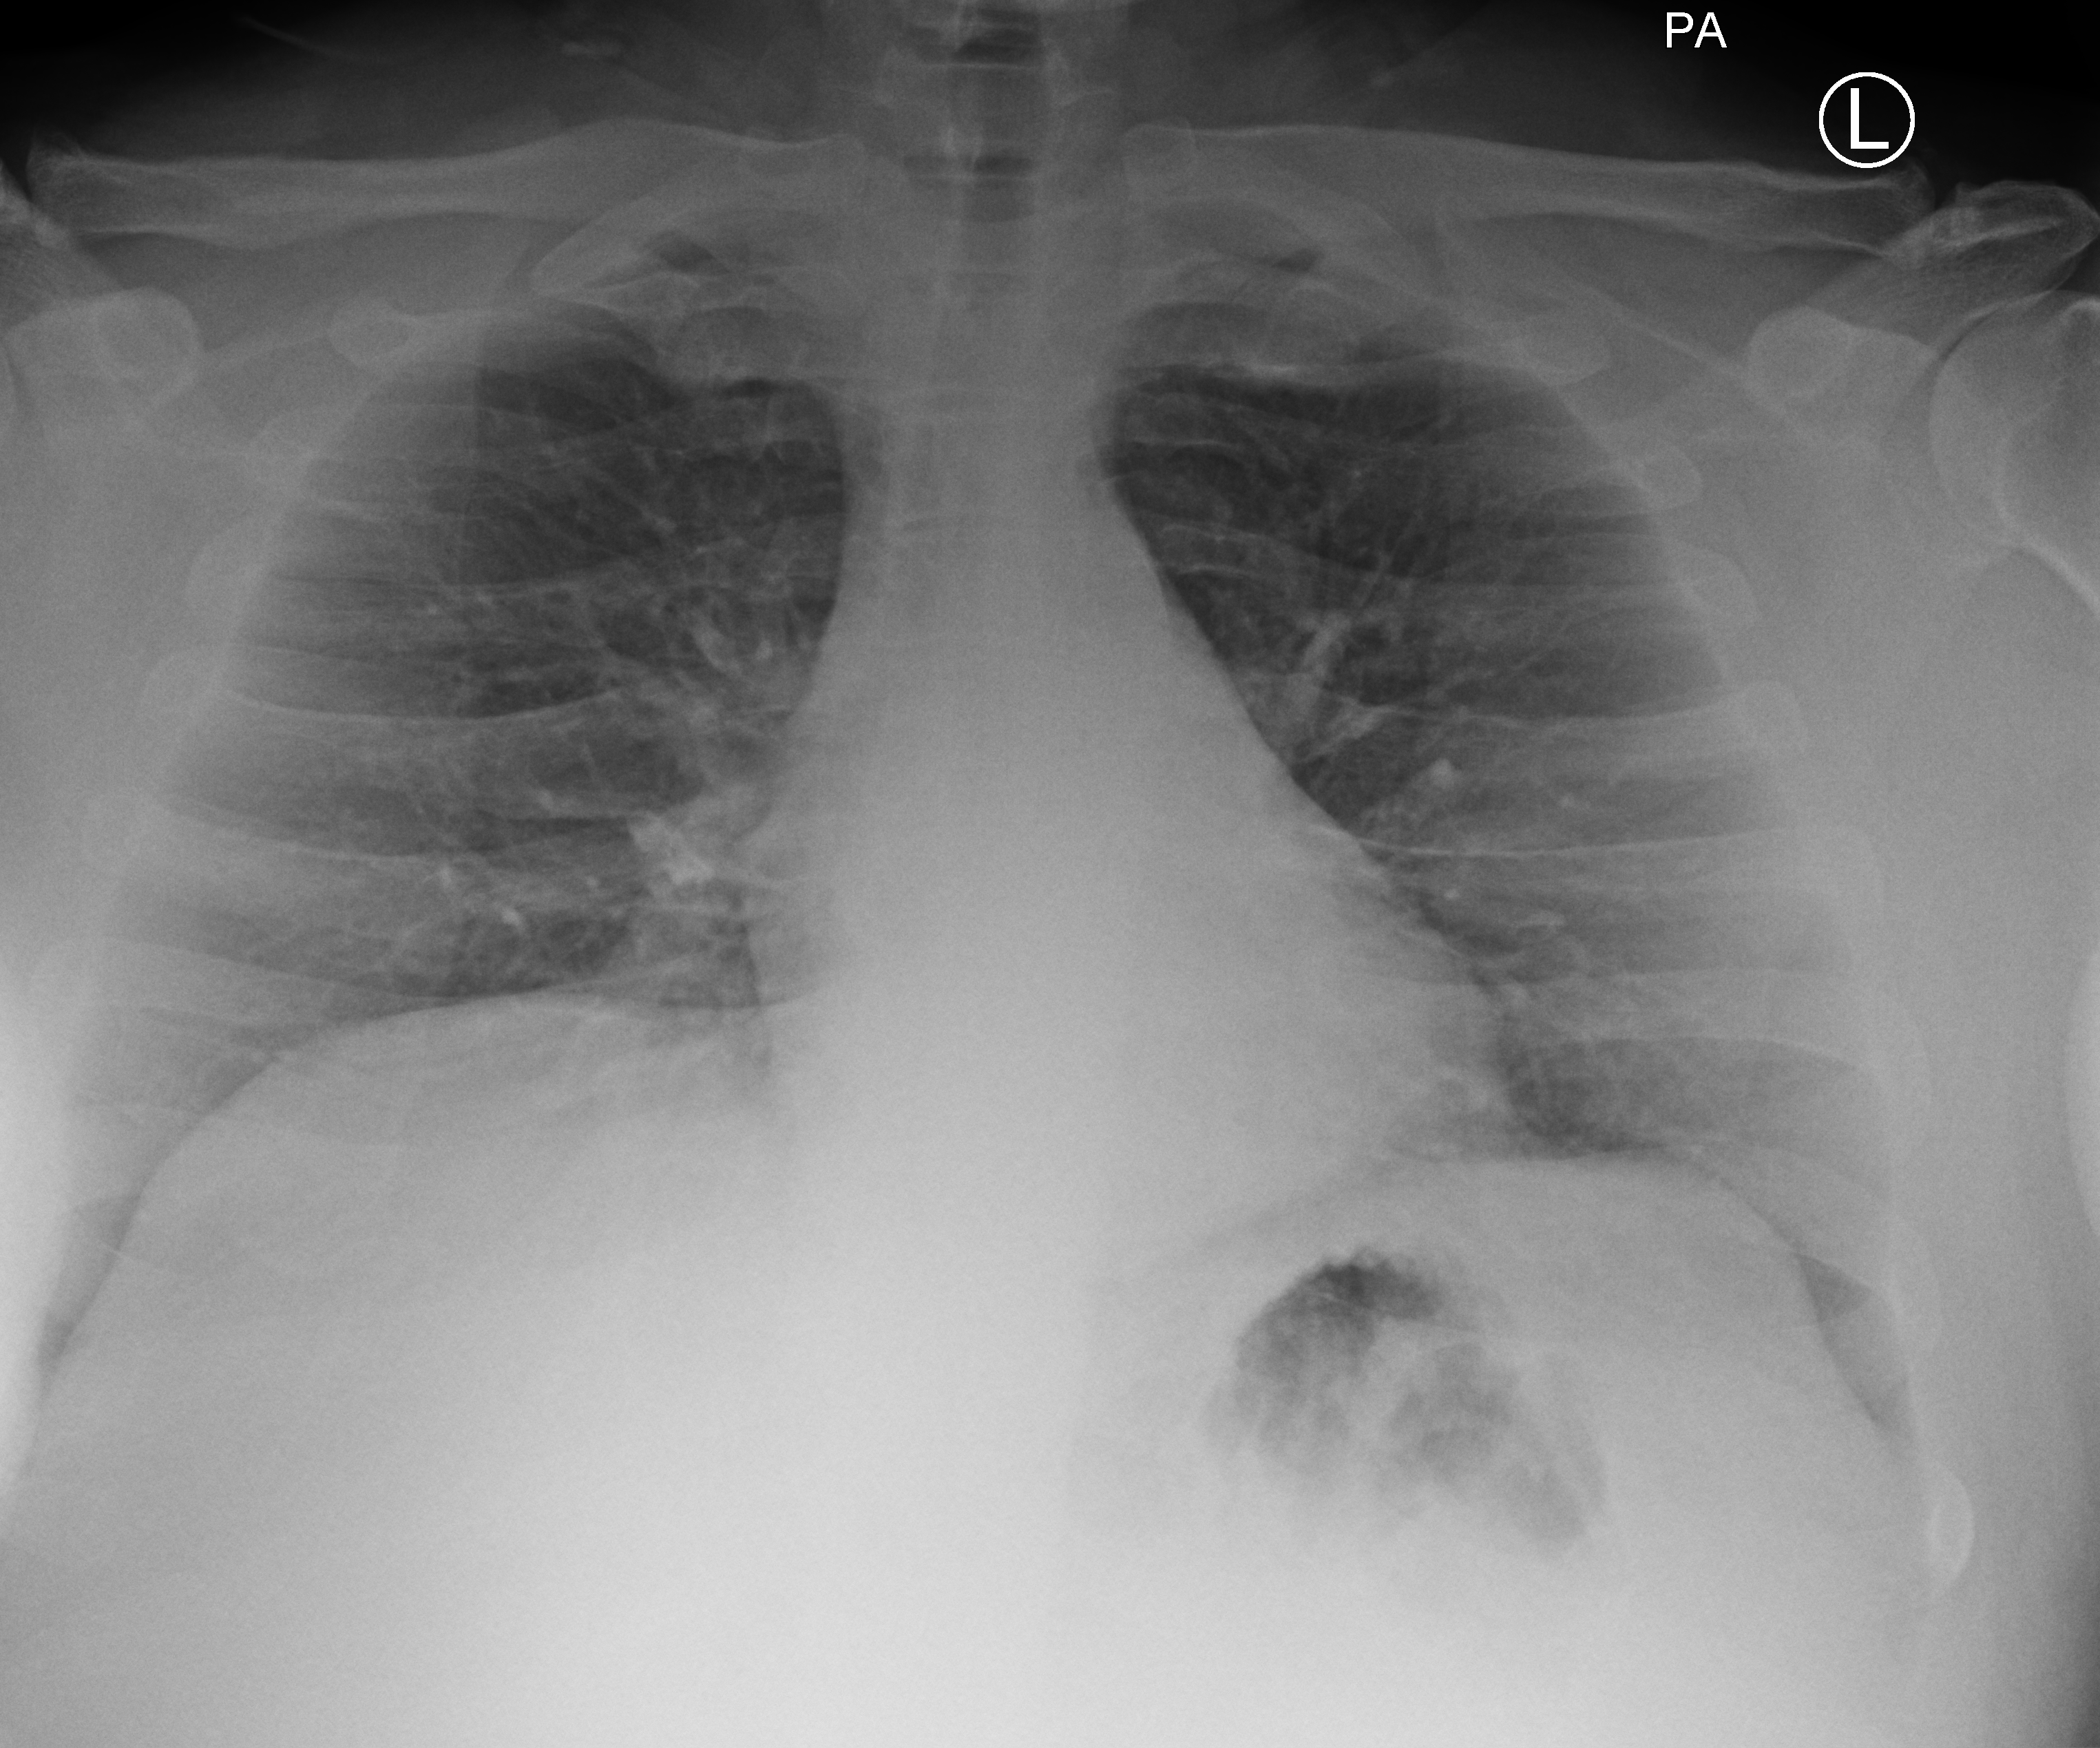
Bedside chest radiograph (computed radiography). Patient hospitalised with COVID-19; male, aged 18–59 years.
Admission-level facts for this patient (not findings on this image; timing relative to this image not recorded): admitted to intensive care during this hospital stay: no; hypertension (admission record): no; other chronic lung disease (admission record): no.